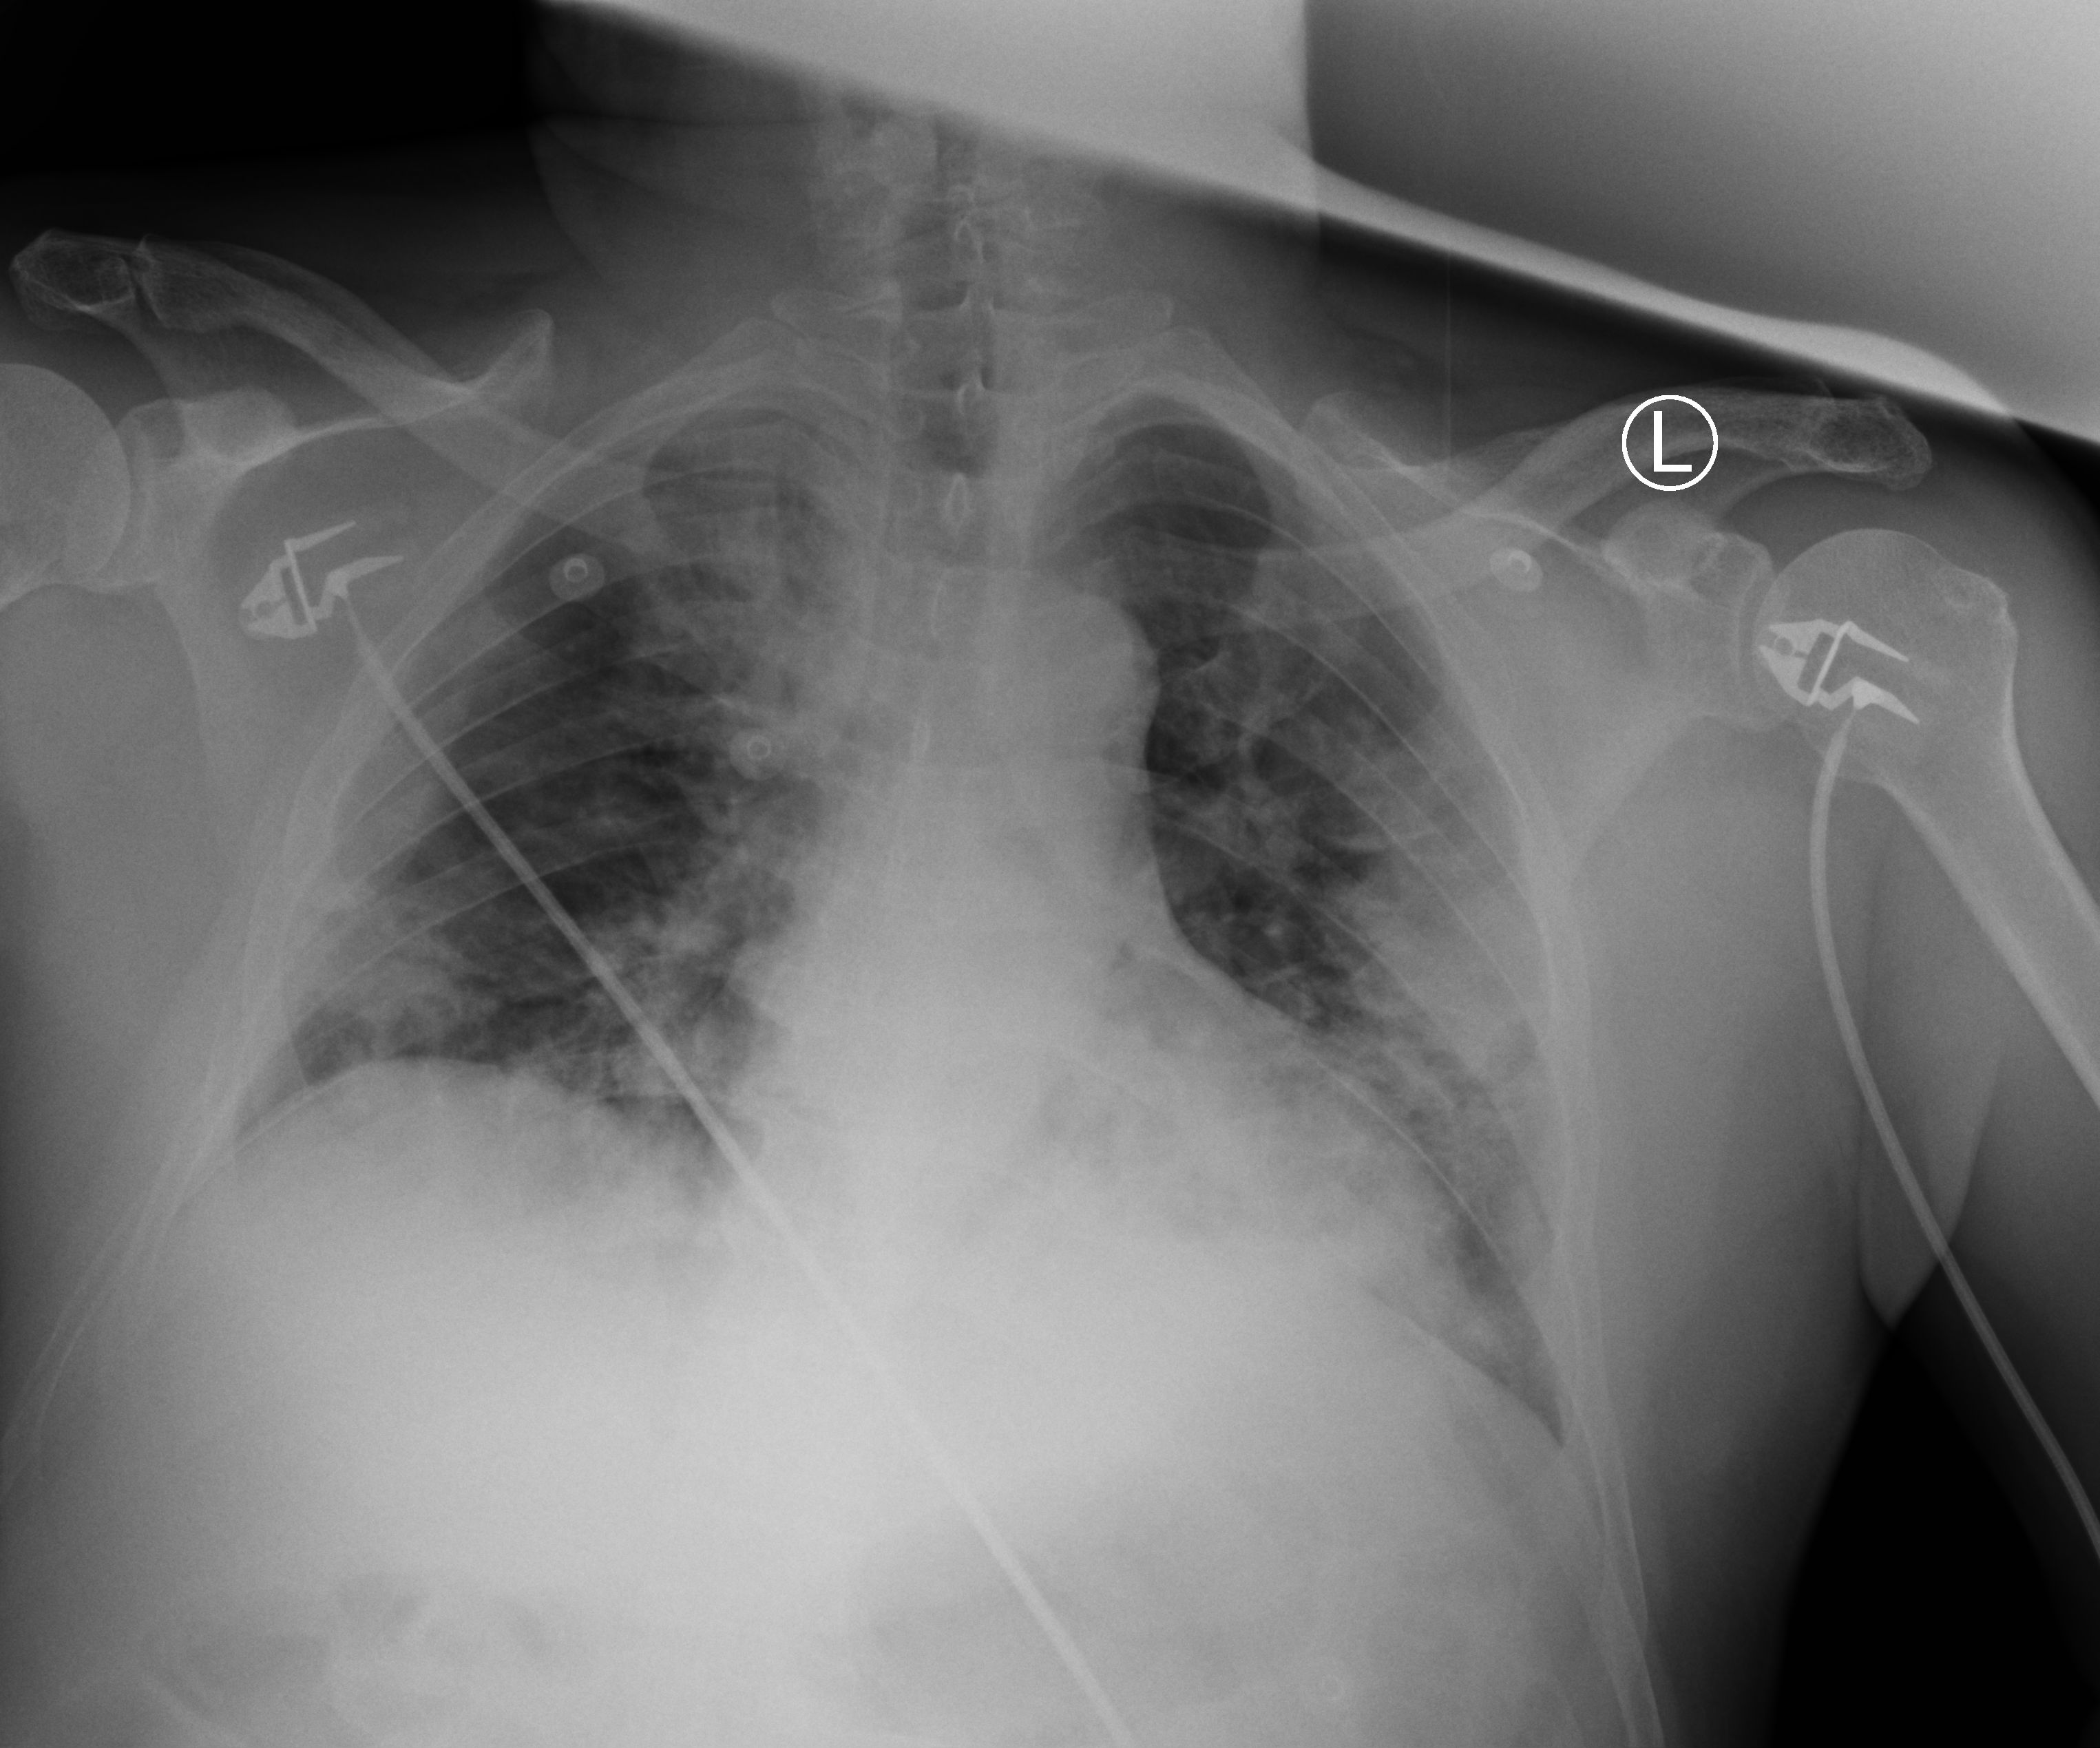
Portable chest radiograph, anteroposterior (AP) projection. Patient hospitalised with COVID-19; male, aged 60–74 years.
From the hospital-stay record, not from the radiograph (when in the stay this image was taken is not recorded):
- chronic kidney disease (admission record): no